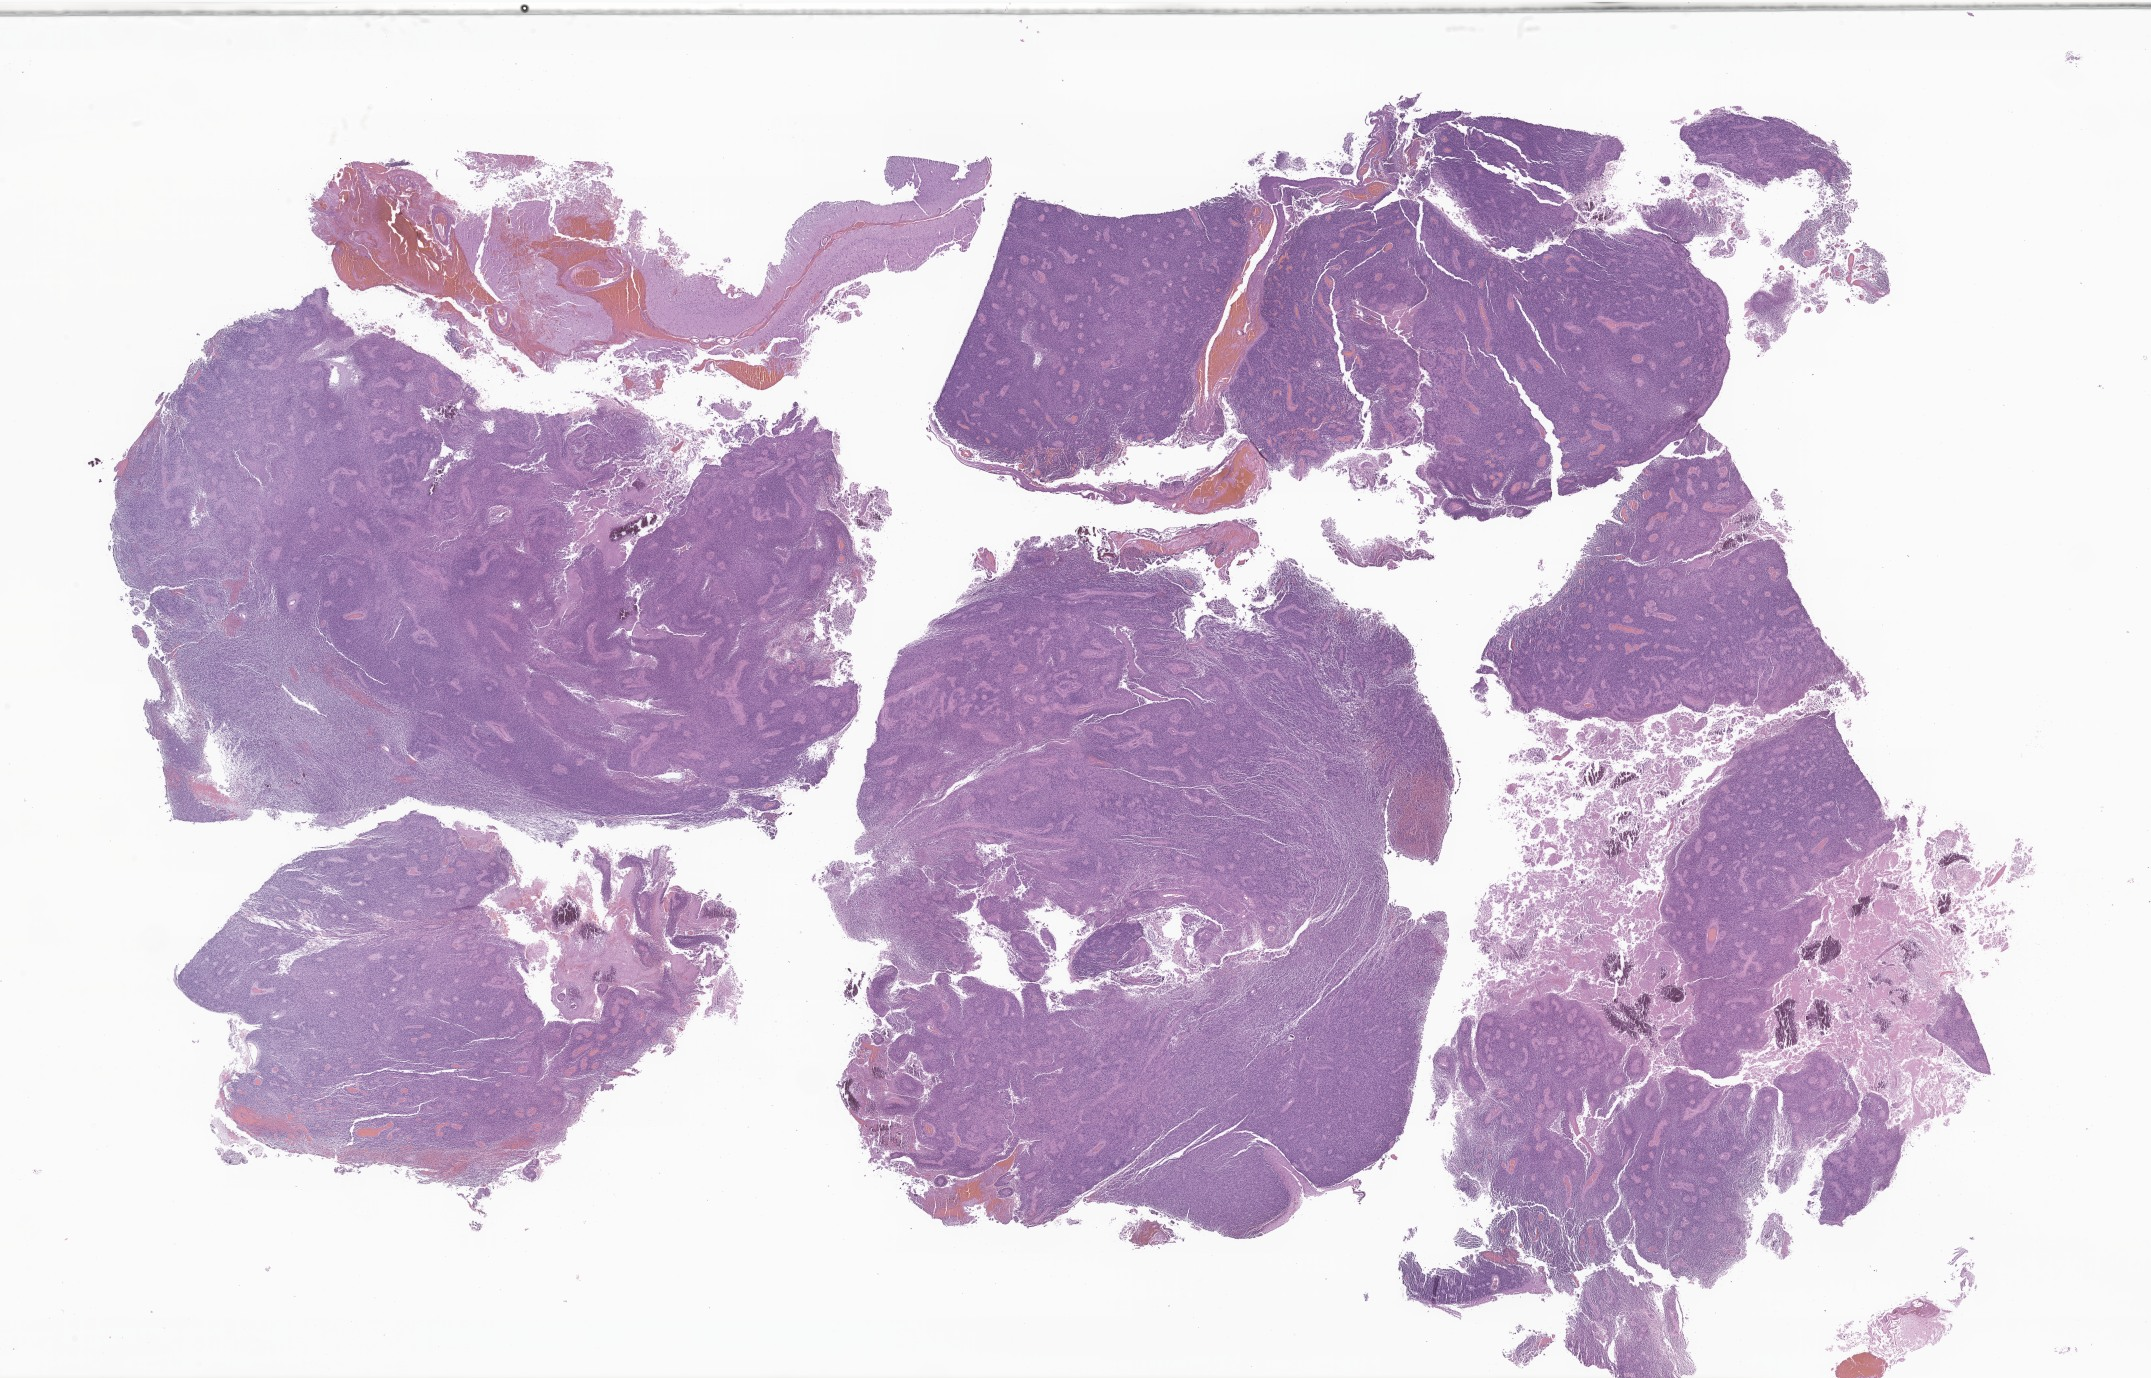
Hematoxylin and eosin (H&E) whole-slide image of tumor tissue from the temporal lobe, low-resolution overview of the scanned area, about 36.3 x 23.2 mm, formalin-fixed, paraffin-embedded (FFPE) tissue. Patient: female, age 159 days.
* diagnosis (ICD-O-3 morphology term): Ependymoma, NOS